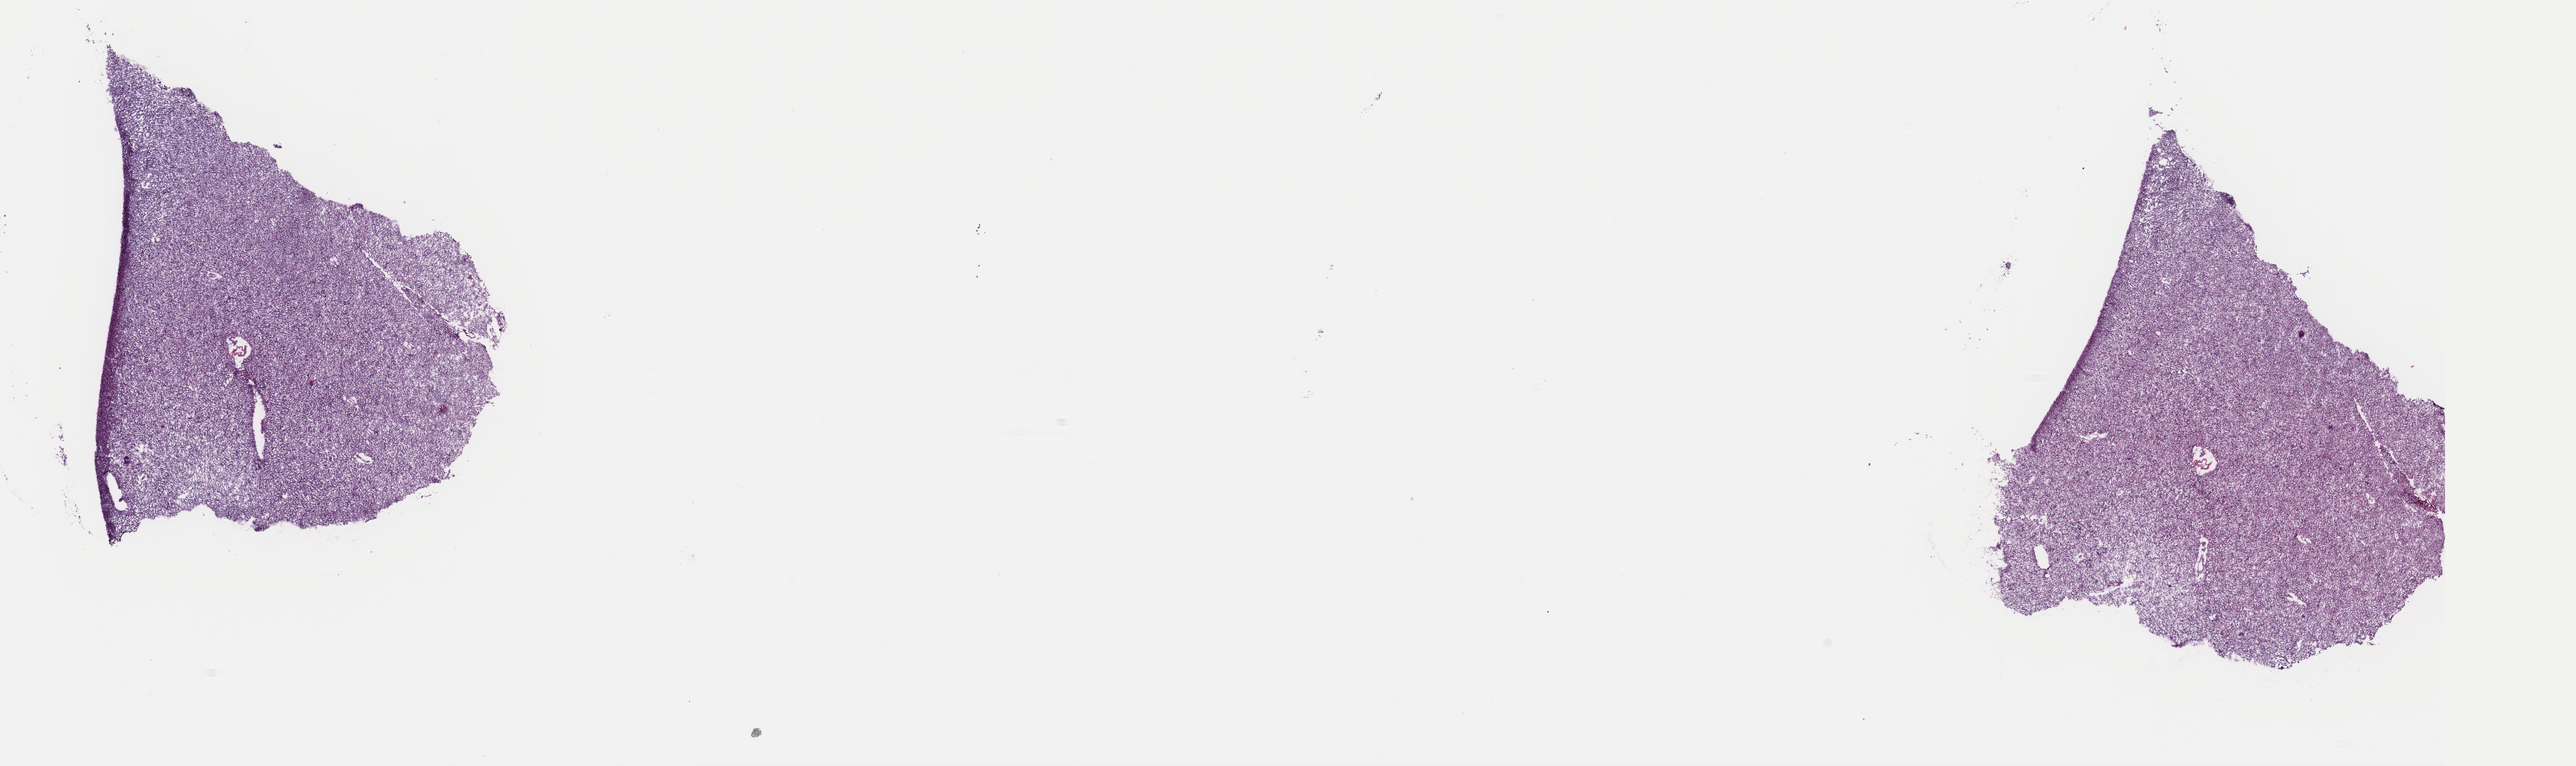
Hematoxylin and eosin (H&E) stained whole-slide image — low-resolution overview of the scanned area, about 28.0 x 8.3 mm (acquisition: 40x scan); frozen section from the top of the tissue portion; brain, primary tumour sample. Male, age 40 years at initial diagnosis. Histologic grade: G2 (moderately differentiated). Slide review estimates, as recorded: tumour cells 60%, tumour nuclei 85%, normal cells 10%, stromal cells 30%, necrosis 0%. Inflammatory infiltration, as recorded: lymphocyte infiltration 0%, monocyte infiltration 0%, neutrophil infiltration 0%.
Diagnosis: Oligodendroglioma, NOS (cerebrum).